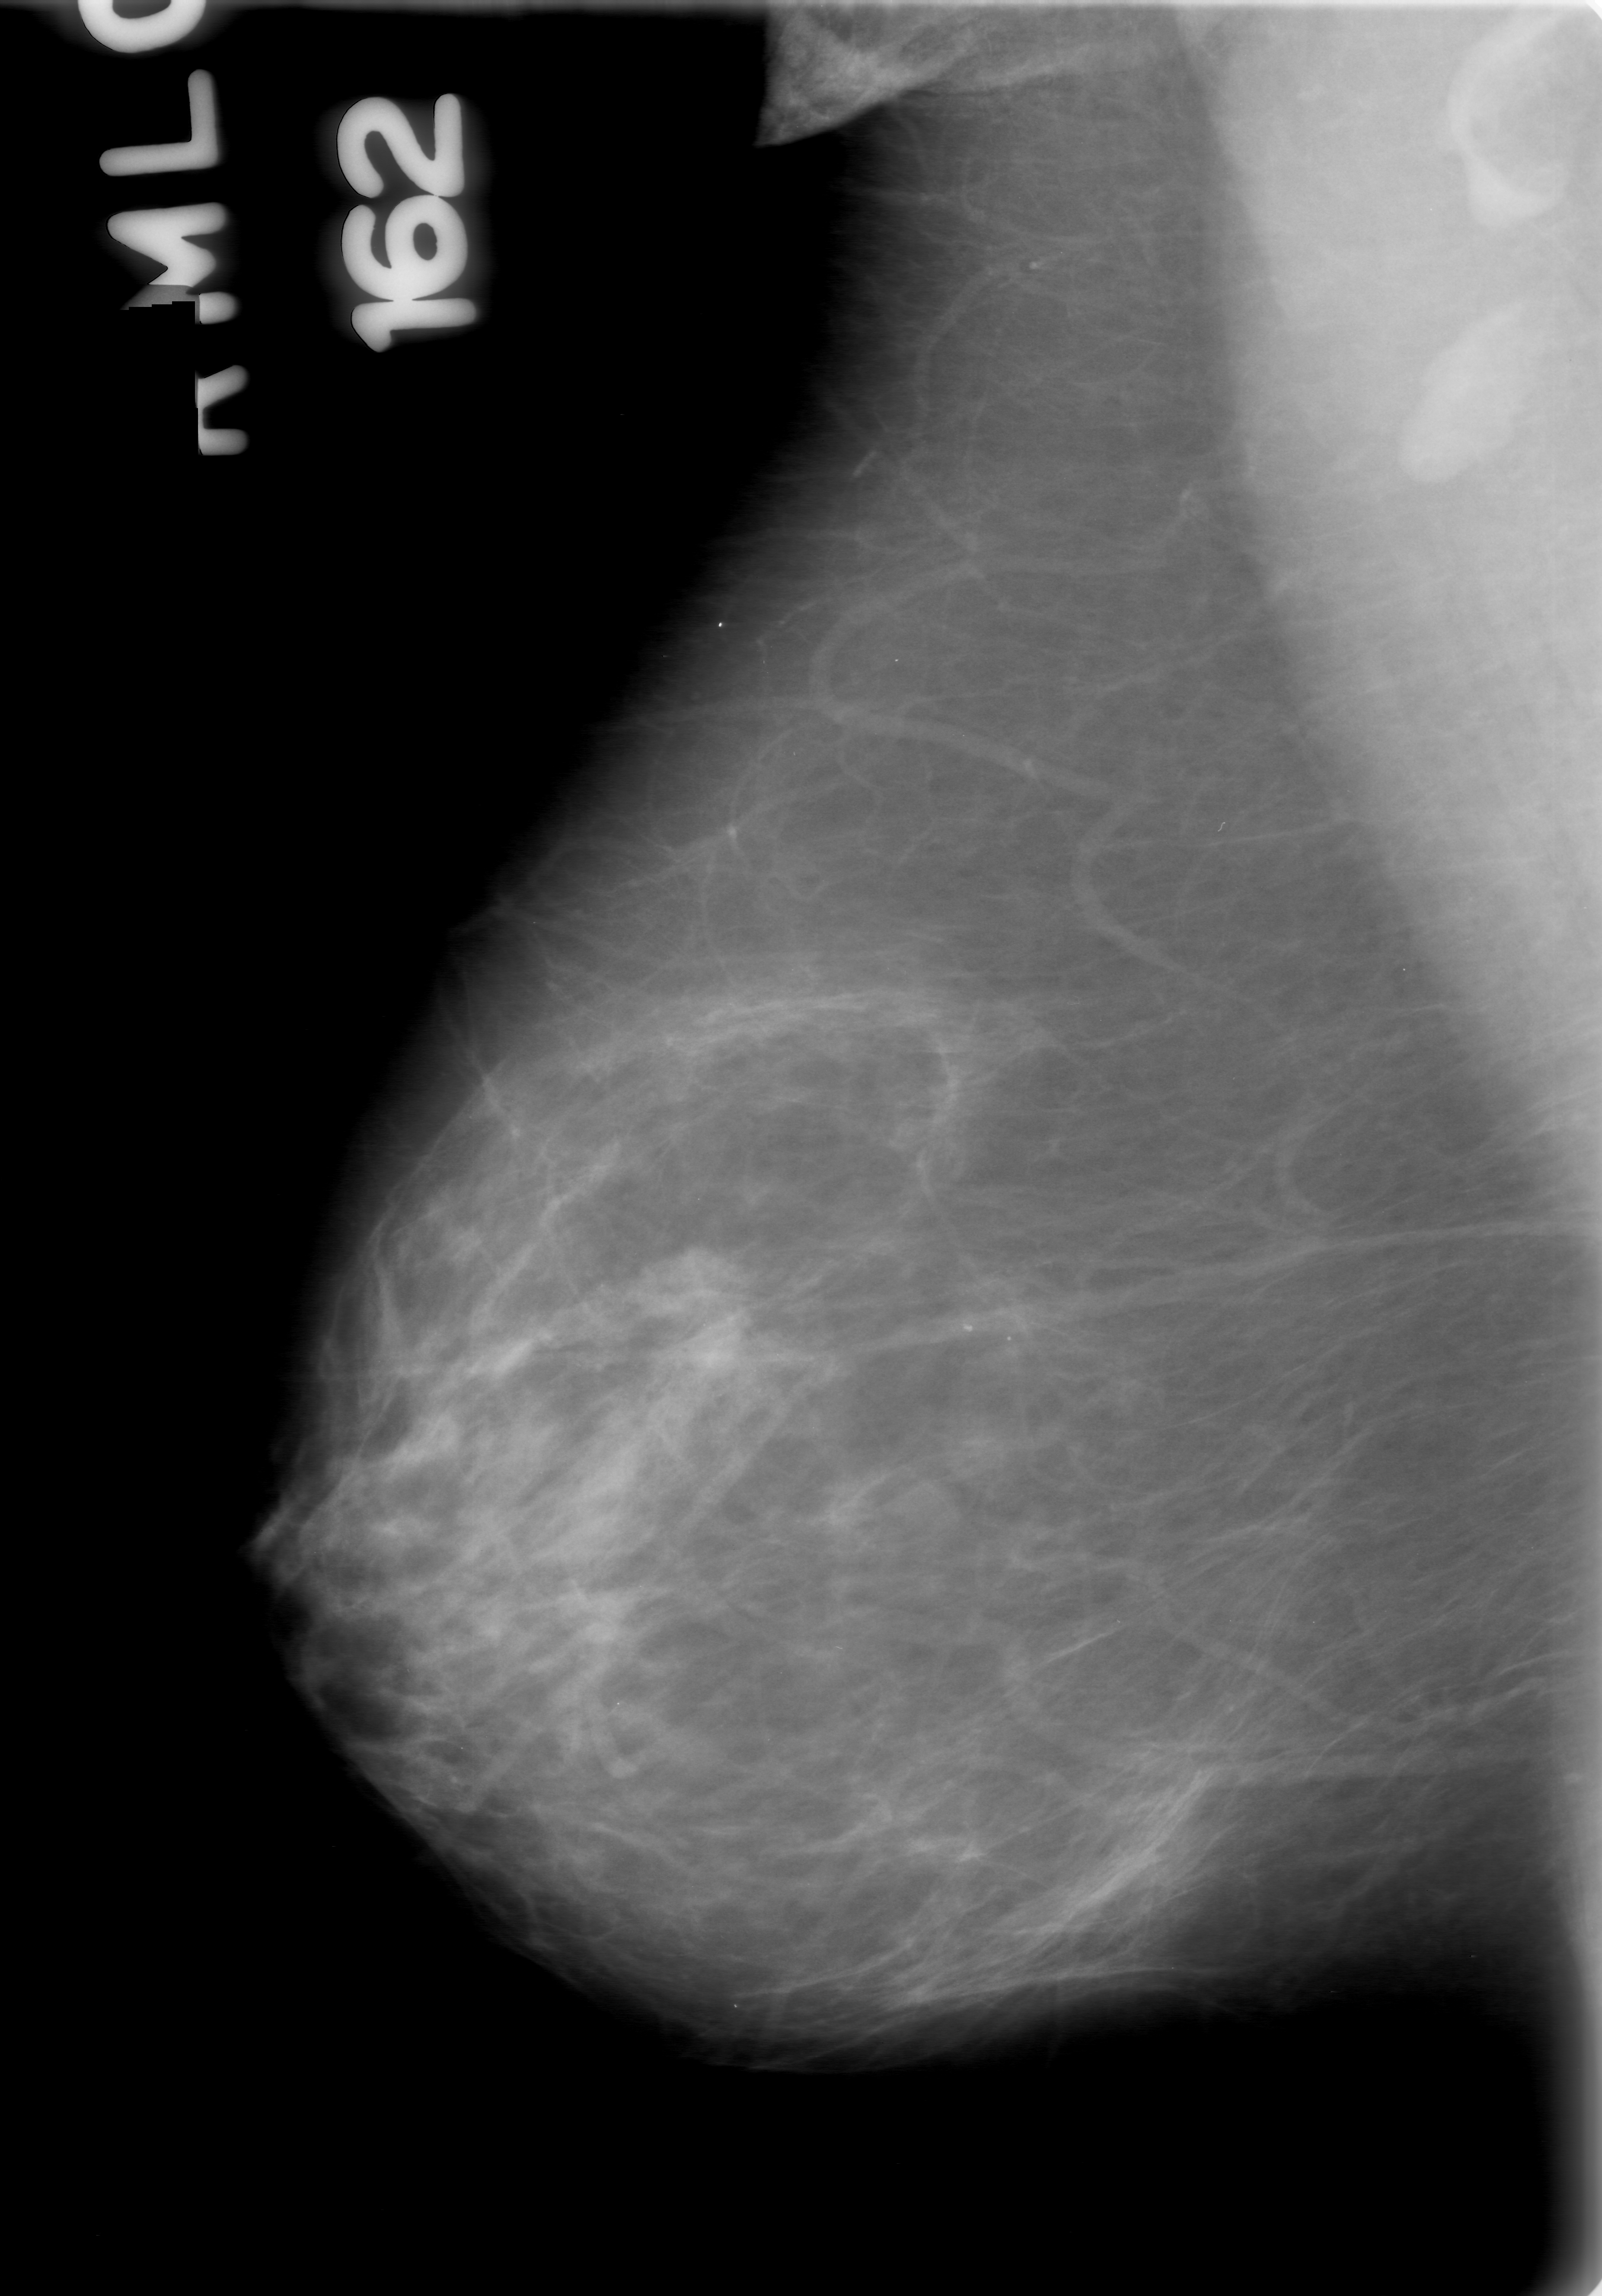
Digitized screen-film mammogram. Right breast. Mediolateral oblique (MLO) view. Breast composition: scattered fibroglandular densities (BI-RADS density category 2 of 4). 1602 × 2296 image matrix.
Marked abnormalities (boxes around the expert regions of interest):
- mass, shape round, margins obscured; BI-RADS assessment category 0 (incomplete: needs additional imaging); subtlety rating 4 on a 1 (subtle) to 5 (obvious) scale; pathology (as recorded): benign: bounding box (x1, y1, x2, y2) in pixels: (645, 1297, 795, 1439)